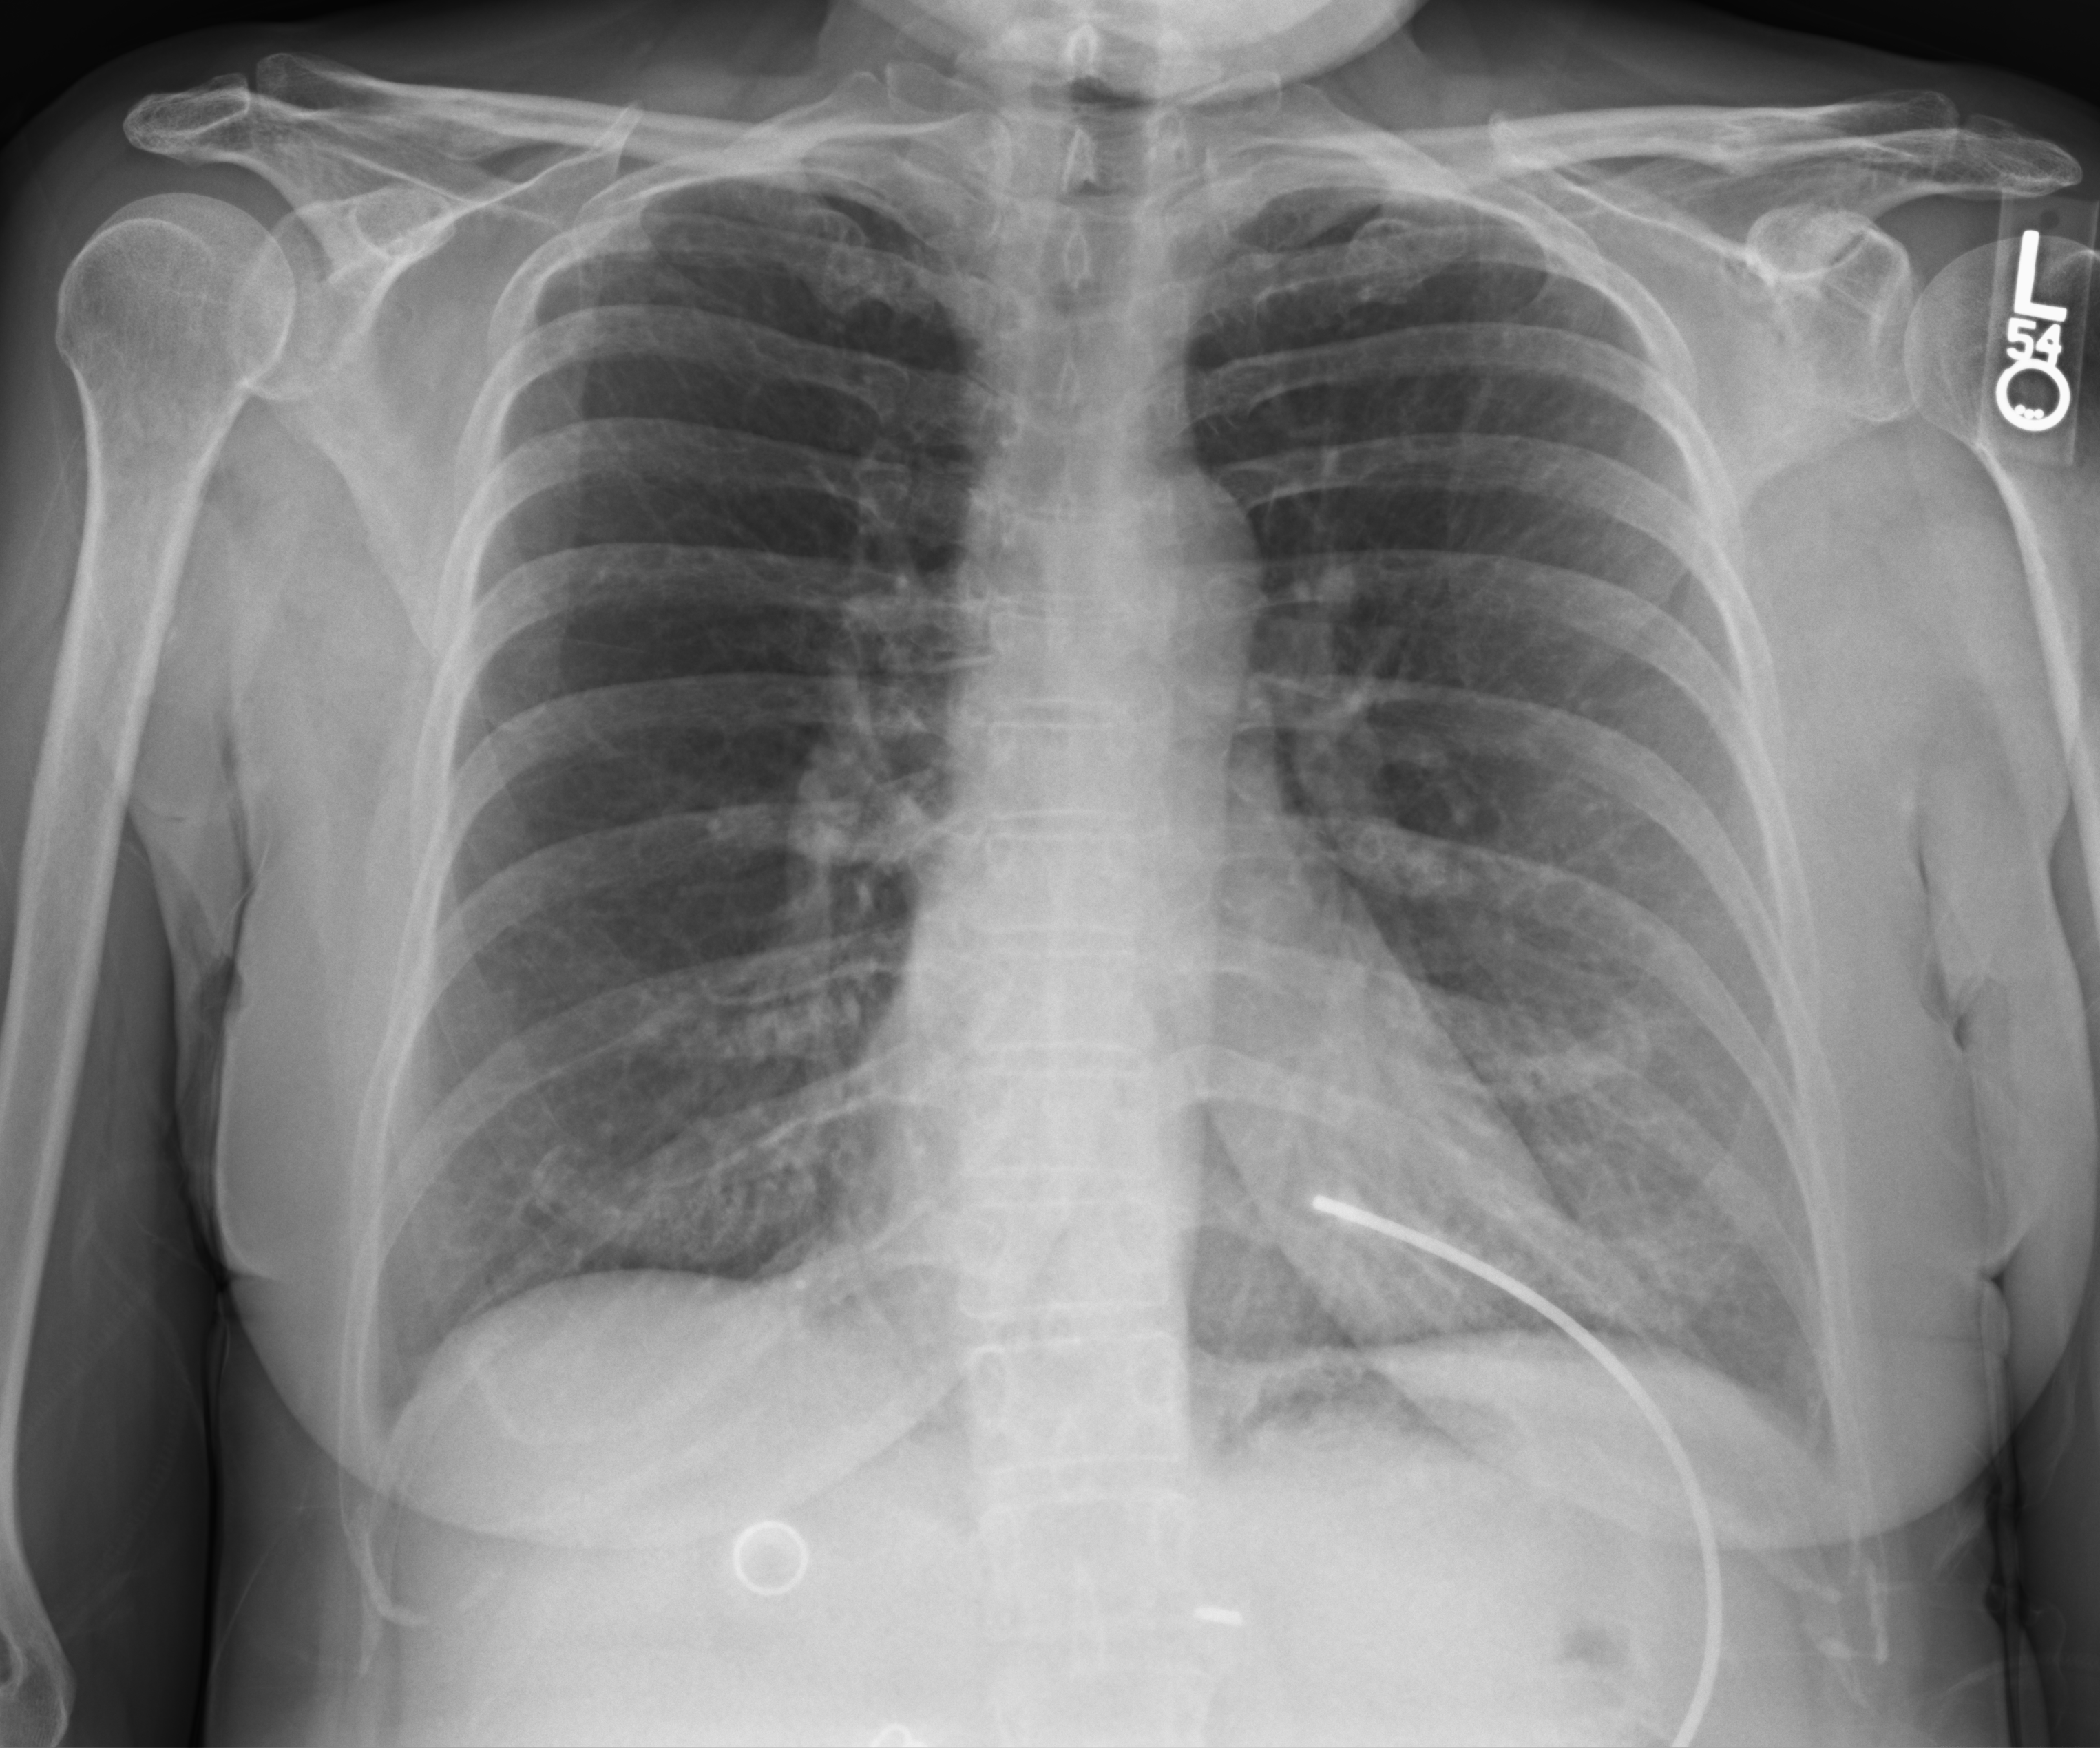
Bedside chest radiograph (computed radiography), anteroposterior (AP) projection. Female patient hospitalised with COVID-19, age 60–74 years.
Hospital-stay facts (about this admission, not read from this image; timing relative to this image not recorded): mechanically ventilated during this hospital stay: no; admitted to intensive care during this hospital stay: no.